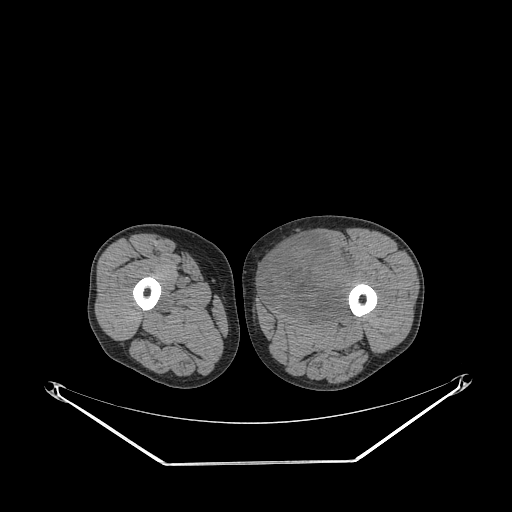
CT of an extremity soft-tissue mass (from a PET/CT study), one axial slice. Reconstruction kernel STANDARD. 140 kVp. Soft-tissue window (W 400 / L 40 HU). 512 × 512 image matrix, field of view 500 × 500 mm. Male patient. Case-level facts recorded for this patient, not image findings: histological type: pleiomorphic liposarcoma; grade: high; site of the primary tumour: left thigh.
Outlined on this slice (expert contour drawn on MRI and transferred to this co-registered scan by the dataset authors):
- gross tumour volume including surrounding oedema: box from (x=263, y=234) to (x=357, y=320) px
- gross tumour volume (mass): (x=263, y=235)–(x=353, y=320)